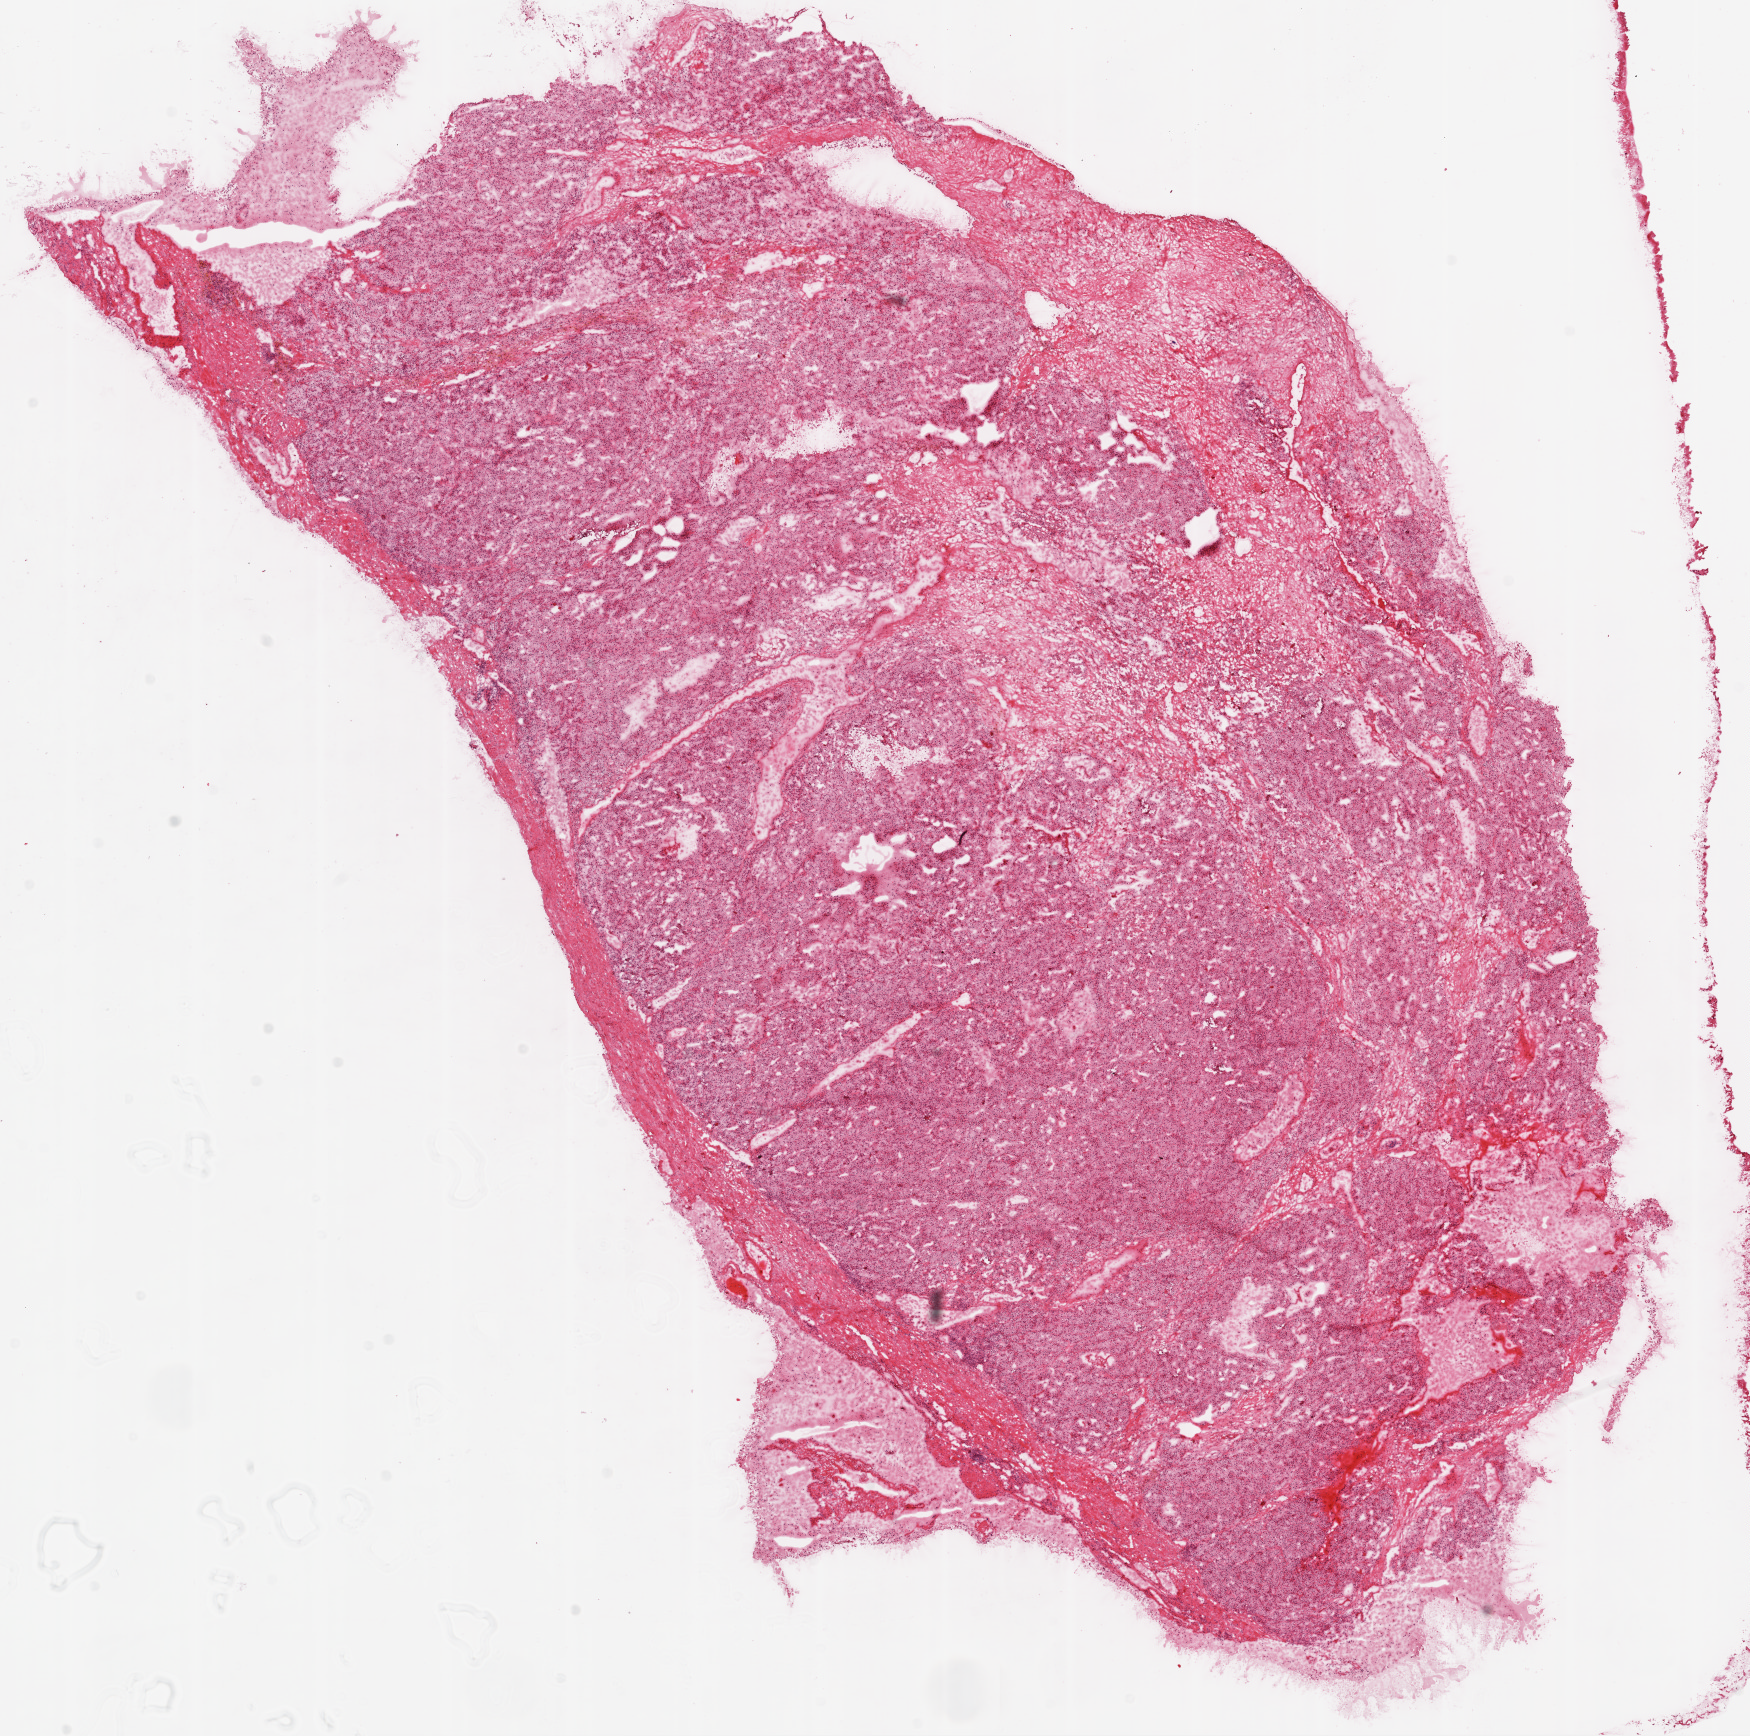
Digitized Hematoxylin and eosin (H&E) stained tissue section (whole slide), a low-resolution overview of the entire scanned area, about 14.0 x 13.9 mm, frozen section from the top of the tissue portion, sample: primary tumour, kidney. Female, age 60 years at initial diagnosis. Histologic grade: G3 (poorly differentiated). Pathologist review of this section (percent, as recorded): tumour cells 80%, tumour nuclei 90%, normal cells 0%, stromal cells 20%, necrosis 0%.
AJCC pathologic stage: III. Histologic diagnosis: Clear cell adenocarcinoma, NOS.